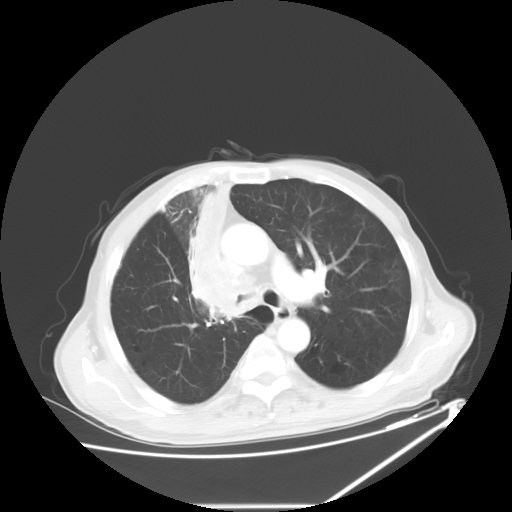
Chest CT, one axial slice. Slice 40 of 60 in the series (ordered by position). 120 kVp. Lung window (W 1500 / L -600 HU). 512 × 512 image matrix, field of view 410 × 410 mm. Male patient, age 73 years. From the clinical record (not read from this slice): clinical TNM (as recorded): T2a N1 M0.
Structures marked on this image (bounding box drawn by a radiologist):
- lung tumour (recorded histology: squamous cell carcinoma): bounding box <187,171,265,321> (left, top, right, bottom; pixels)